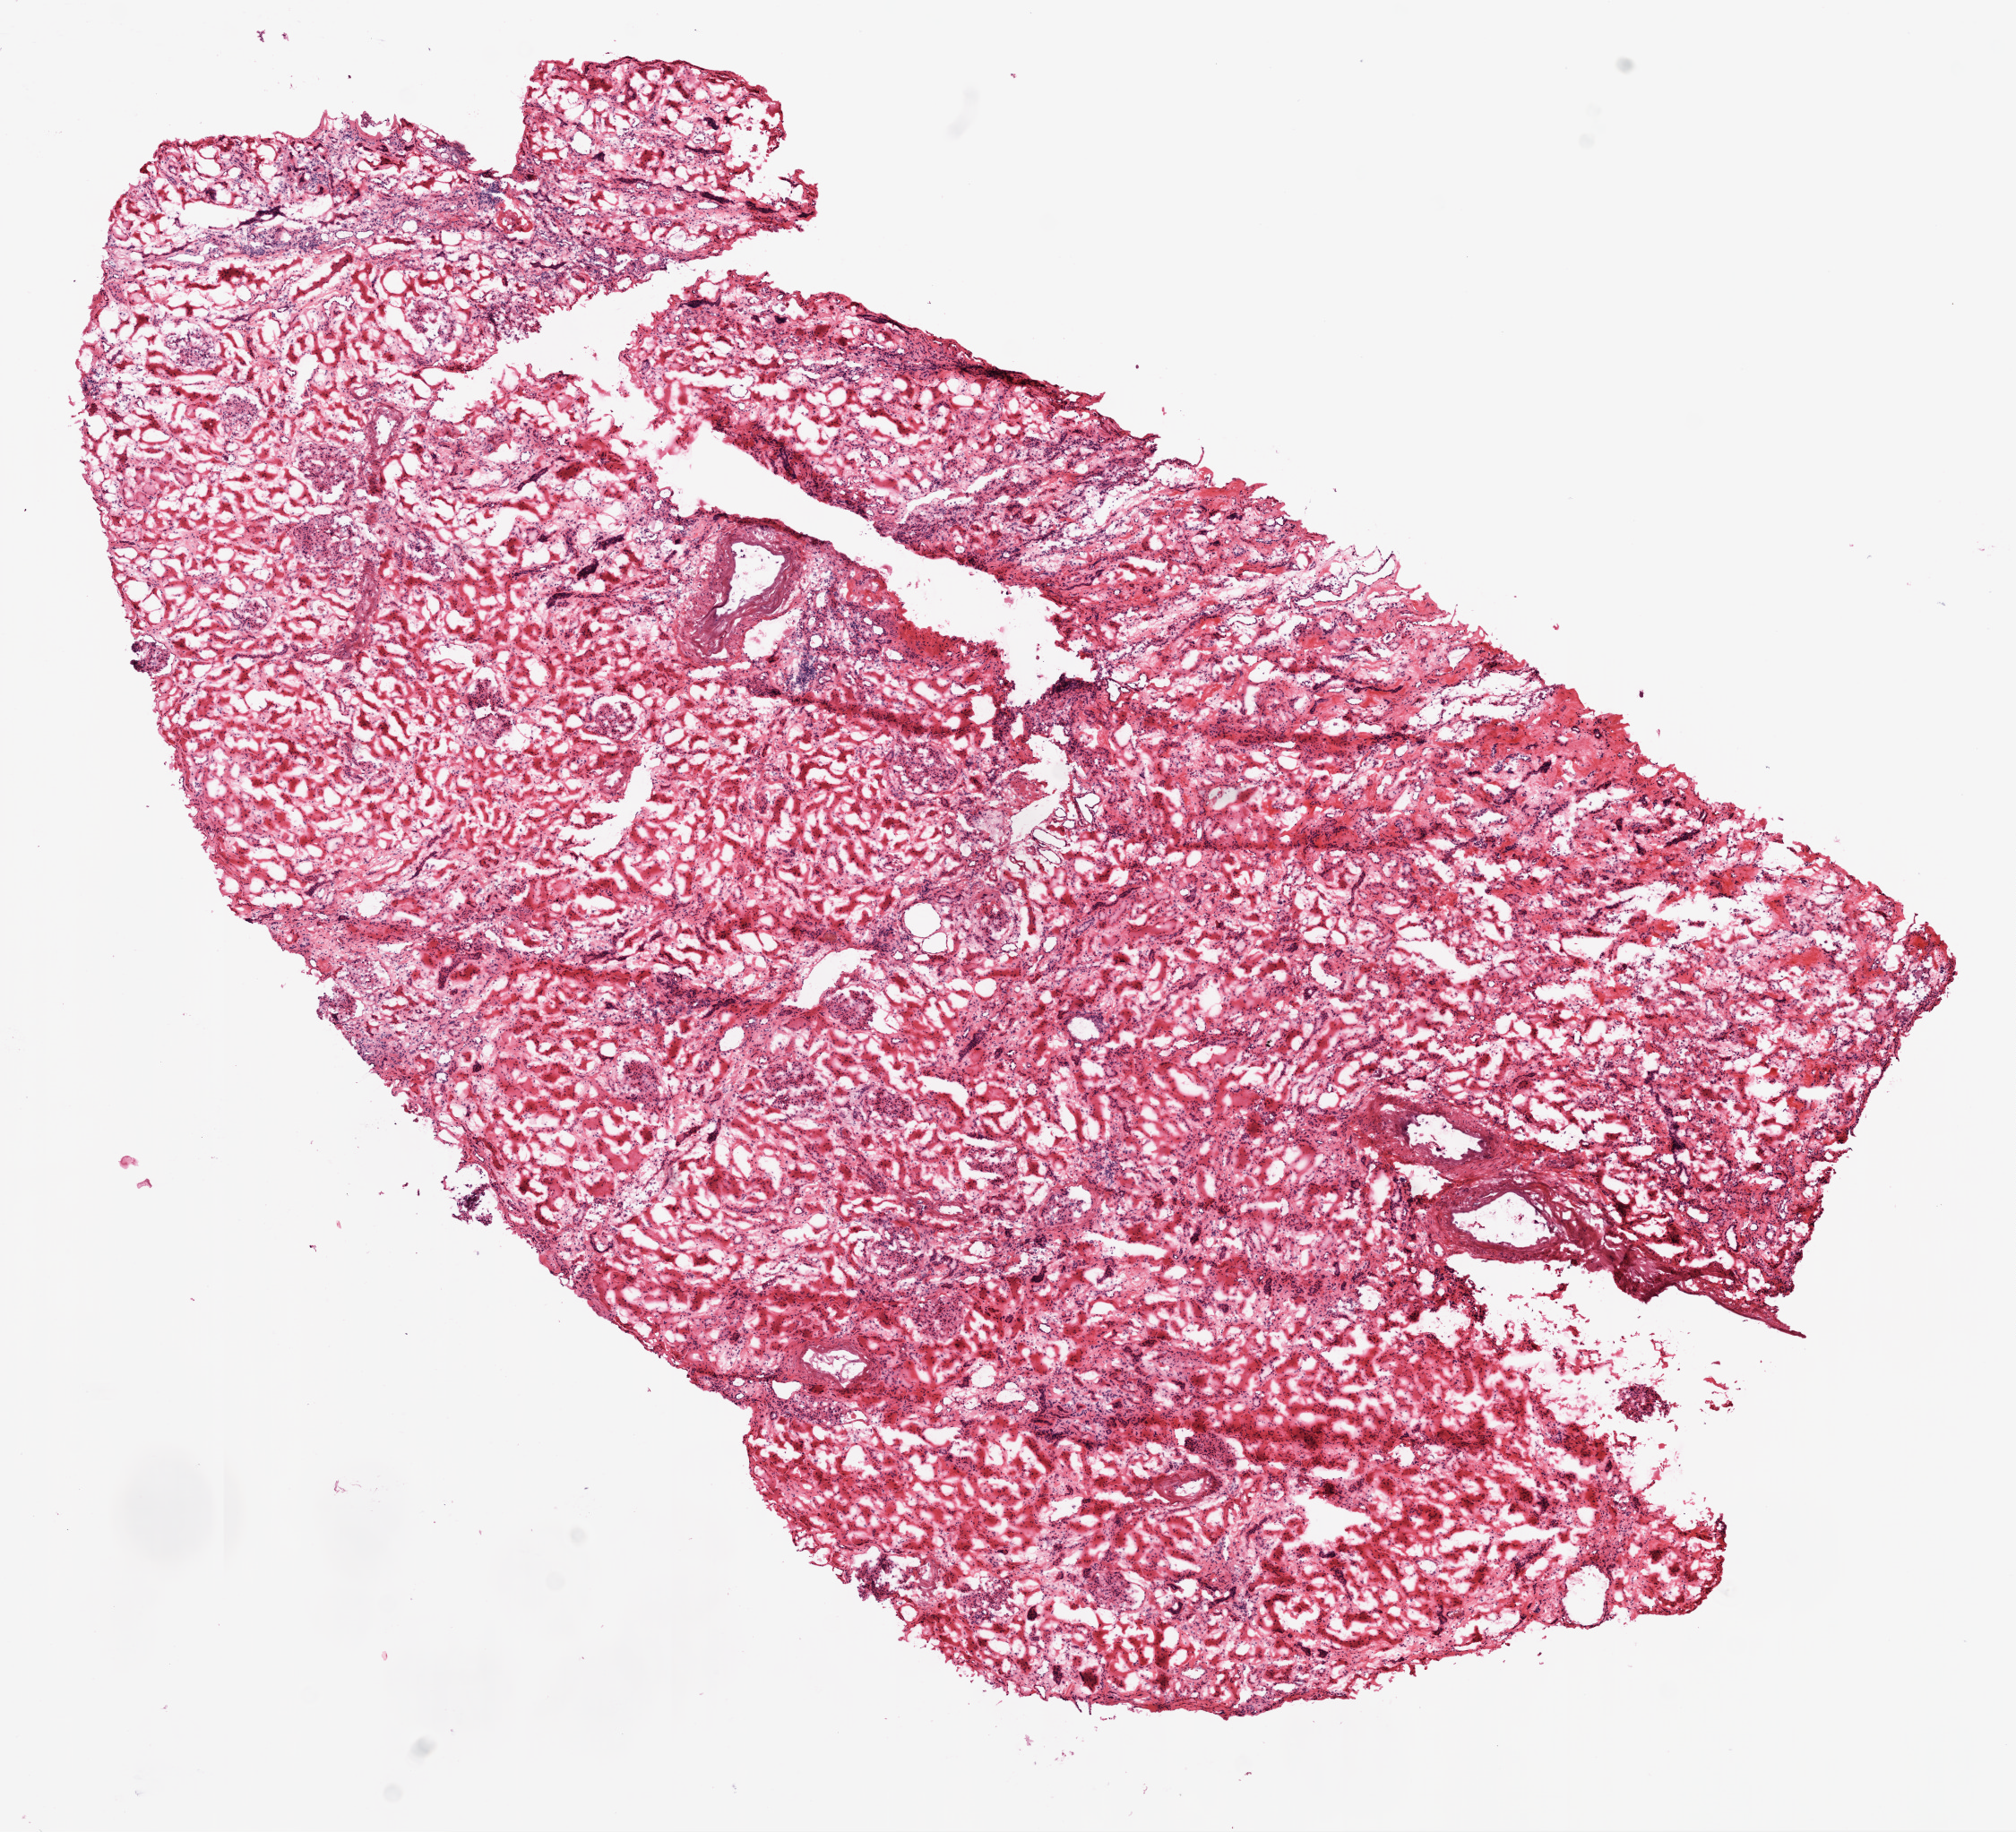
Hematoxylin and eosin (H&E) stained whole-slide image — a low-resolution overview of the entire scanned area, about 9.0 x 8.2 mm (from a 20x scan), frozen section, solid tissue normal (non-tumour tissue) sample from the kidney. Patient sex: male.
This section: solid tissue normal sample (biorepository sample class). Patient diagnosis: Clear cell adenocarcinoma, NOS.